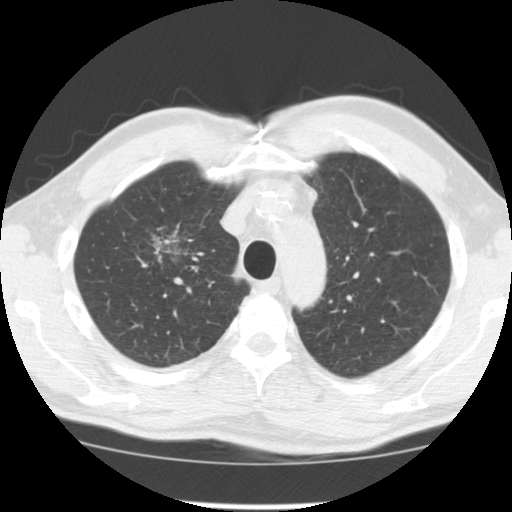
Axial slice from a low-dose chest CT screening exam. Third screening round (two years after baseline). Lung window (W 1500 / L -600 HU). Standard (soft-tissue) reconstruction kernel (STANDARD). 120 kVp. Slice 31 of 128 in the series. Male, age 64 years at enrolment. Former smoker at enrolment.
Expert-annotated lung lesion, bounding box <129,215,210,282> (left, top, right, bottom; pixels). The screening reader recorded 3 non-calcified nodules or masses ≥4 mm on this exam (right upper lobe, right lower lobe, left upper lobe); which of them this box marks is not recorded.